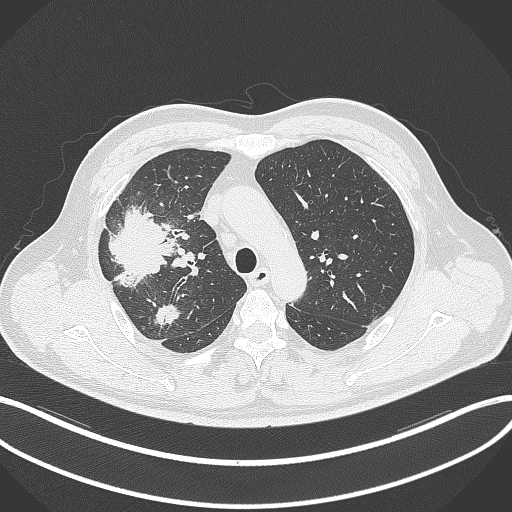
Chest CT, one axial slice; slice 243 of 348 in the series (ordered by position); 120 kVp; lung window (W 1500 / L -600 HU); 512 × 512 image matrix, field of view 400 × 400 mm. Patient: male, 55 years. From the clinical record (not read from this slice): clinical TNM (as recorded): T3 N2 M1.
Outlined on this slice (rectangle marked by the reading radiologist):
- lung tumour (recorded histology: adenocarcinoma): bounding box <106,205,179,289> (left, top, right, bottom; pixels)